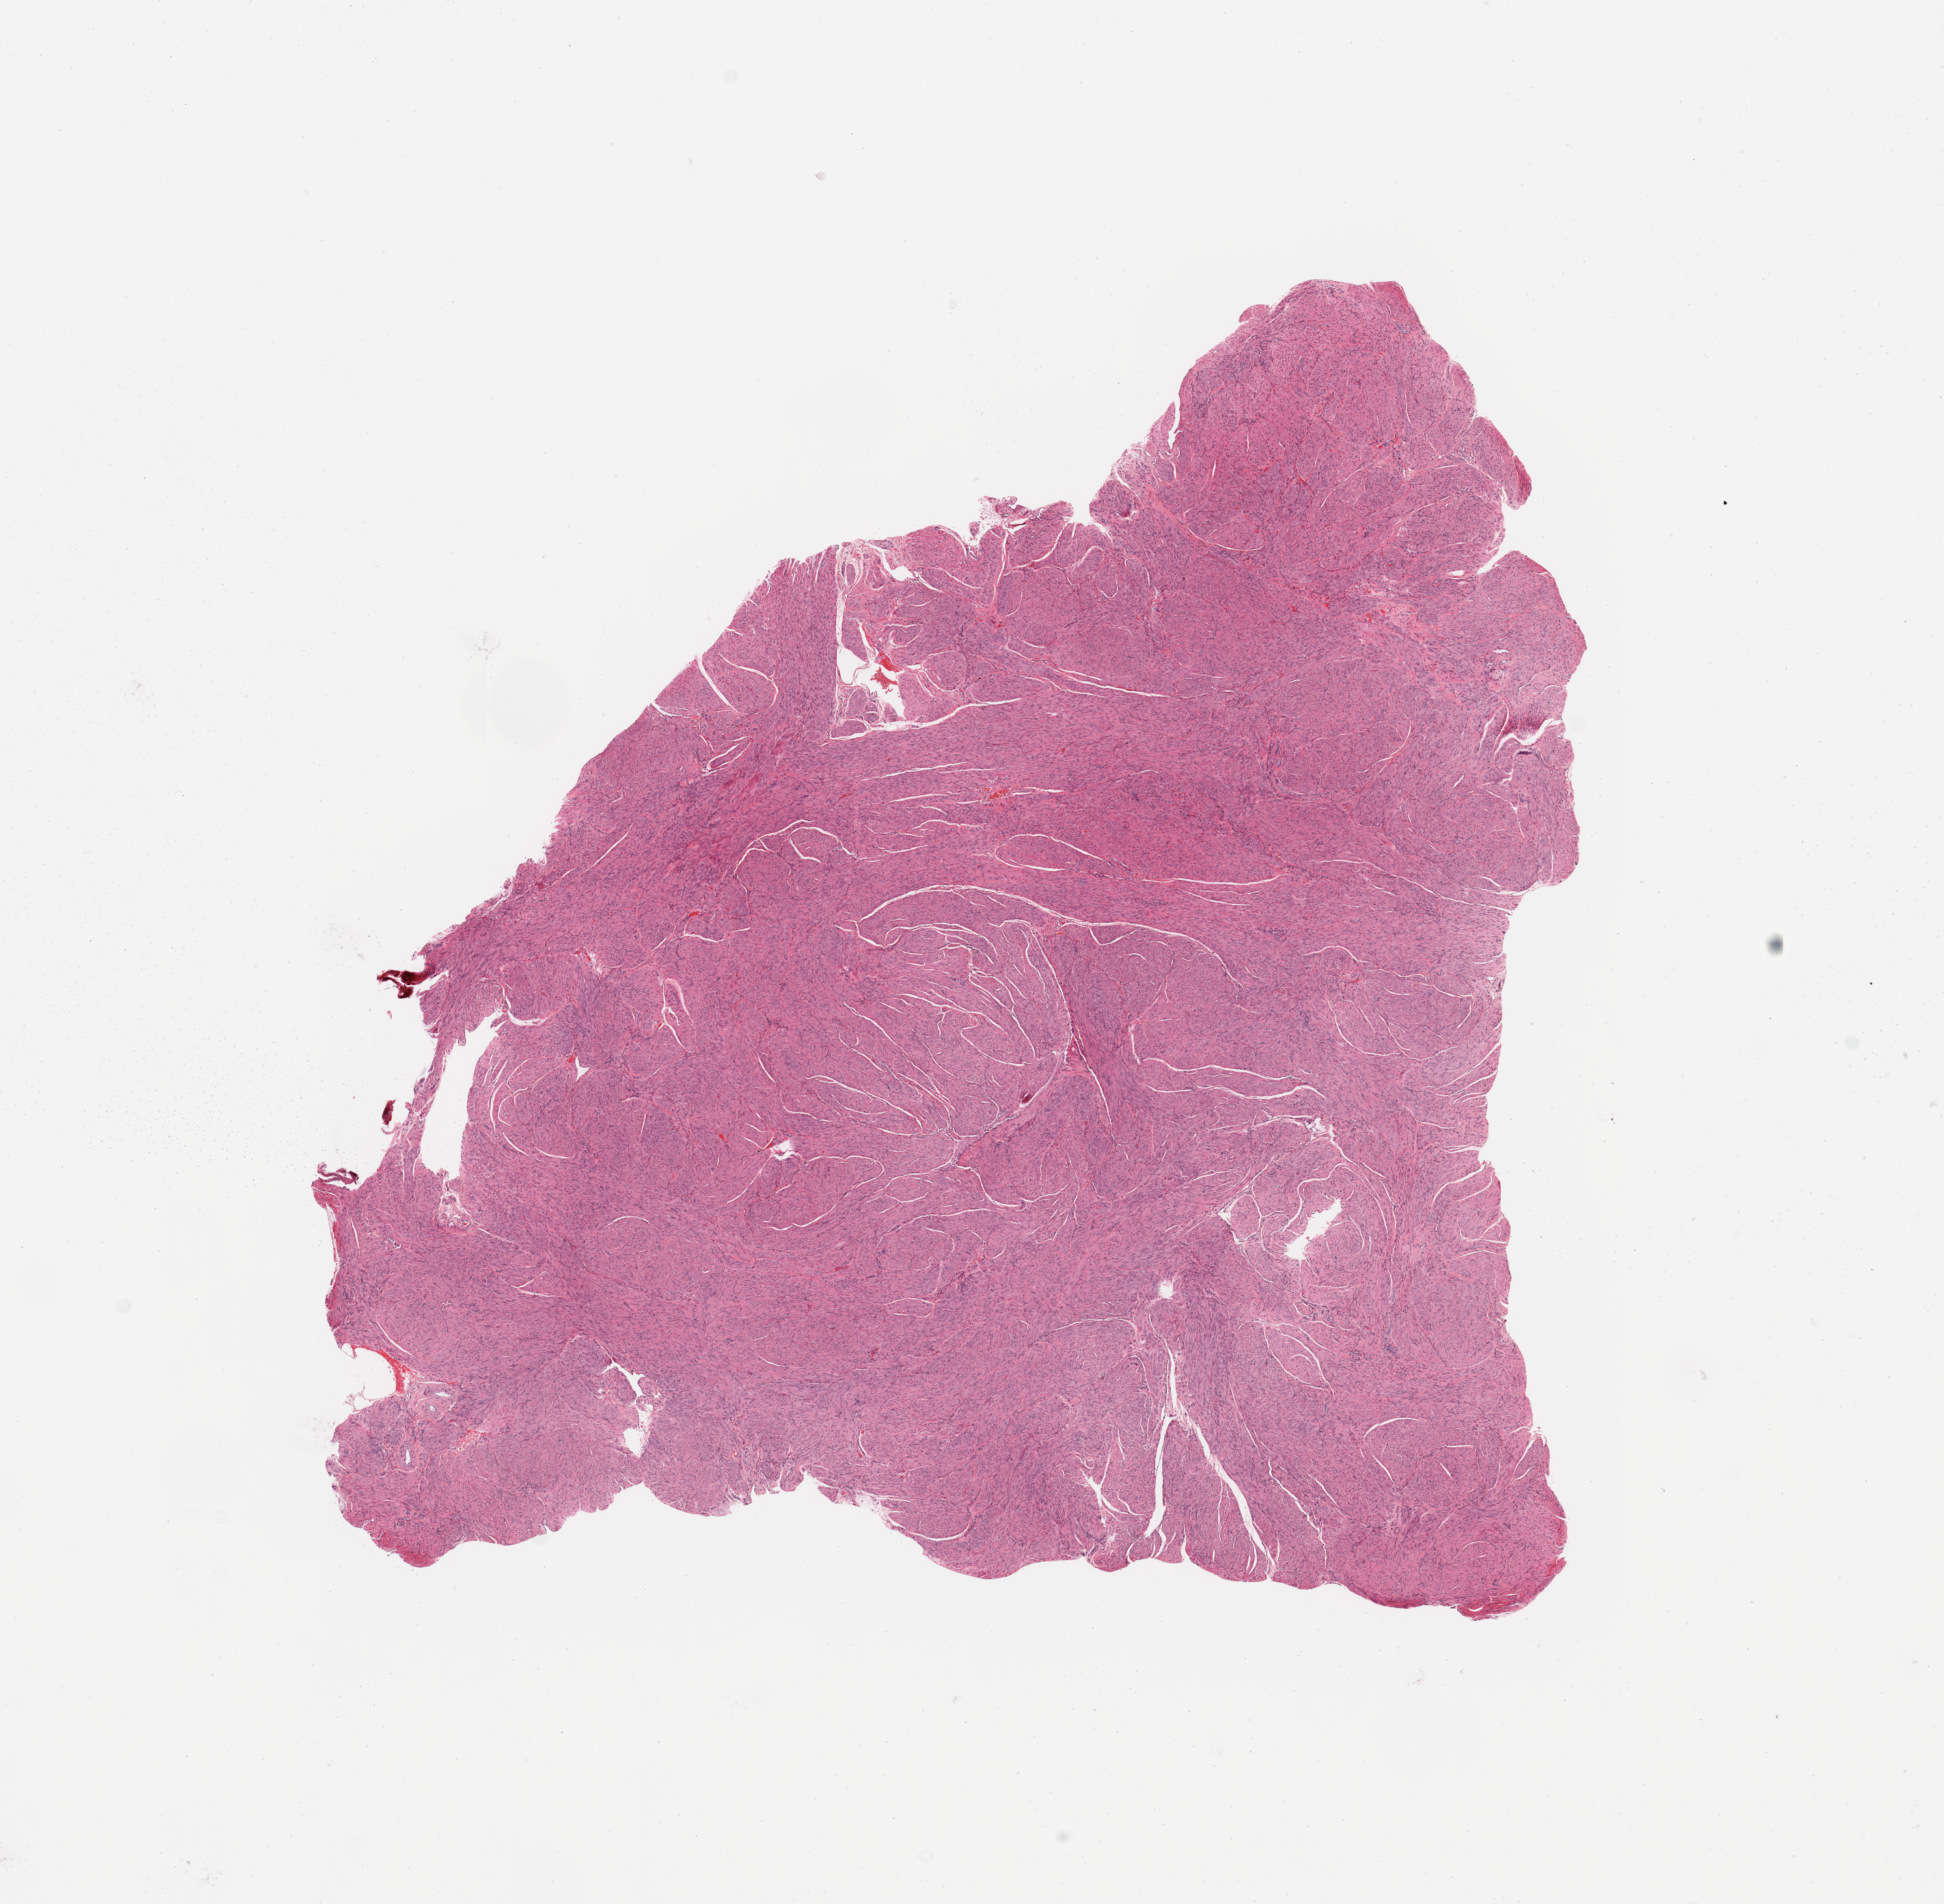
Digitized H&E-stained tissue section (whole slide), whole scanned area (about 11.8 x 11.6 mm) shown as a low-resolution overview. Normal (non-tumour) tissue sample, sampled site: uterus. Female, 60 y/o.
This section: normal (non-tumour) tissue from the same patient. Patient diagnosis: Endometrioid adenocarcinoma, NOS.